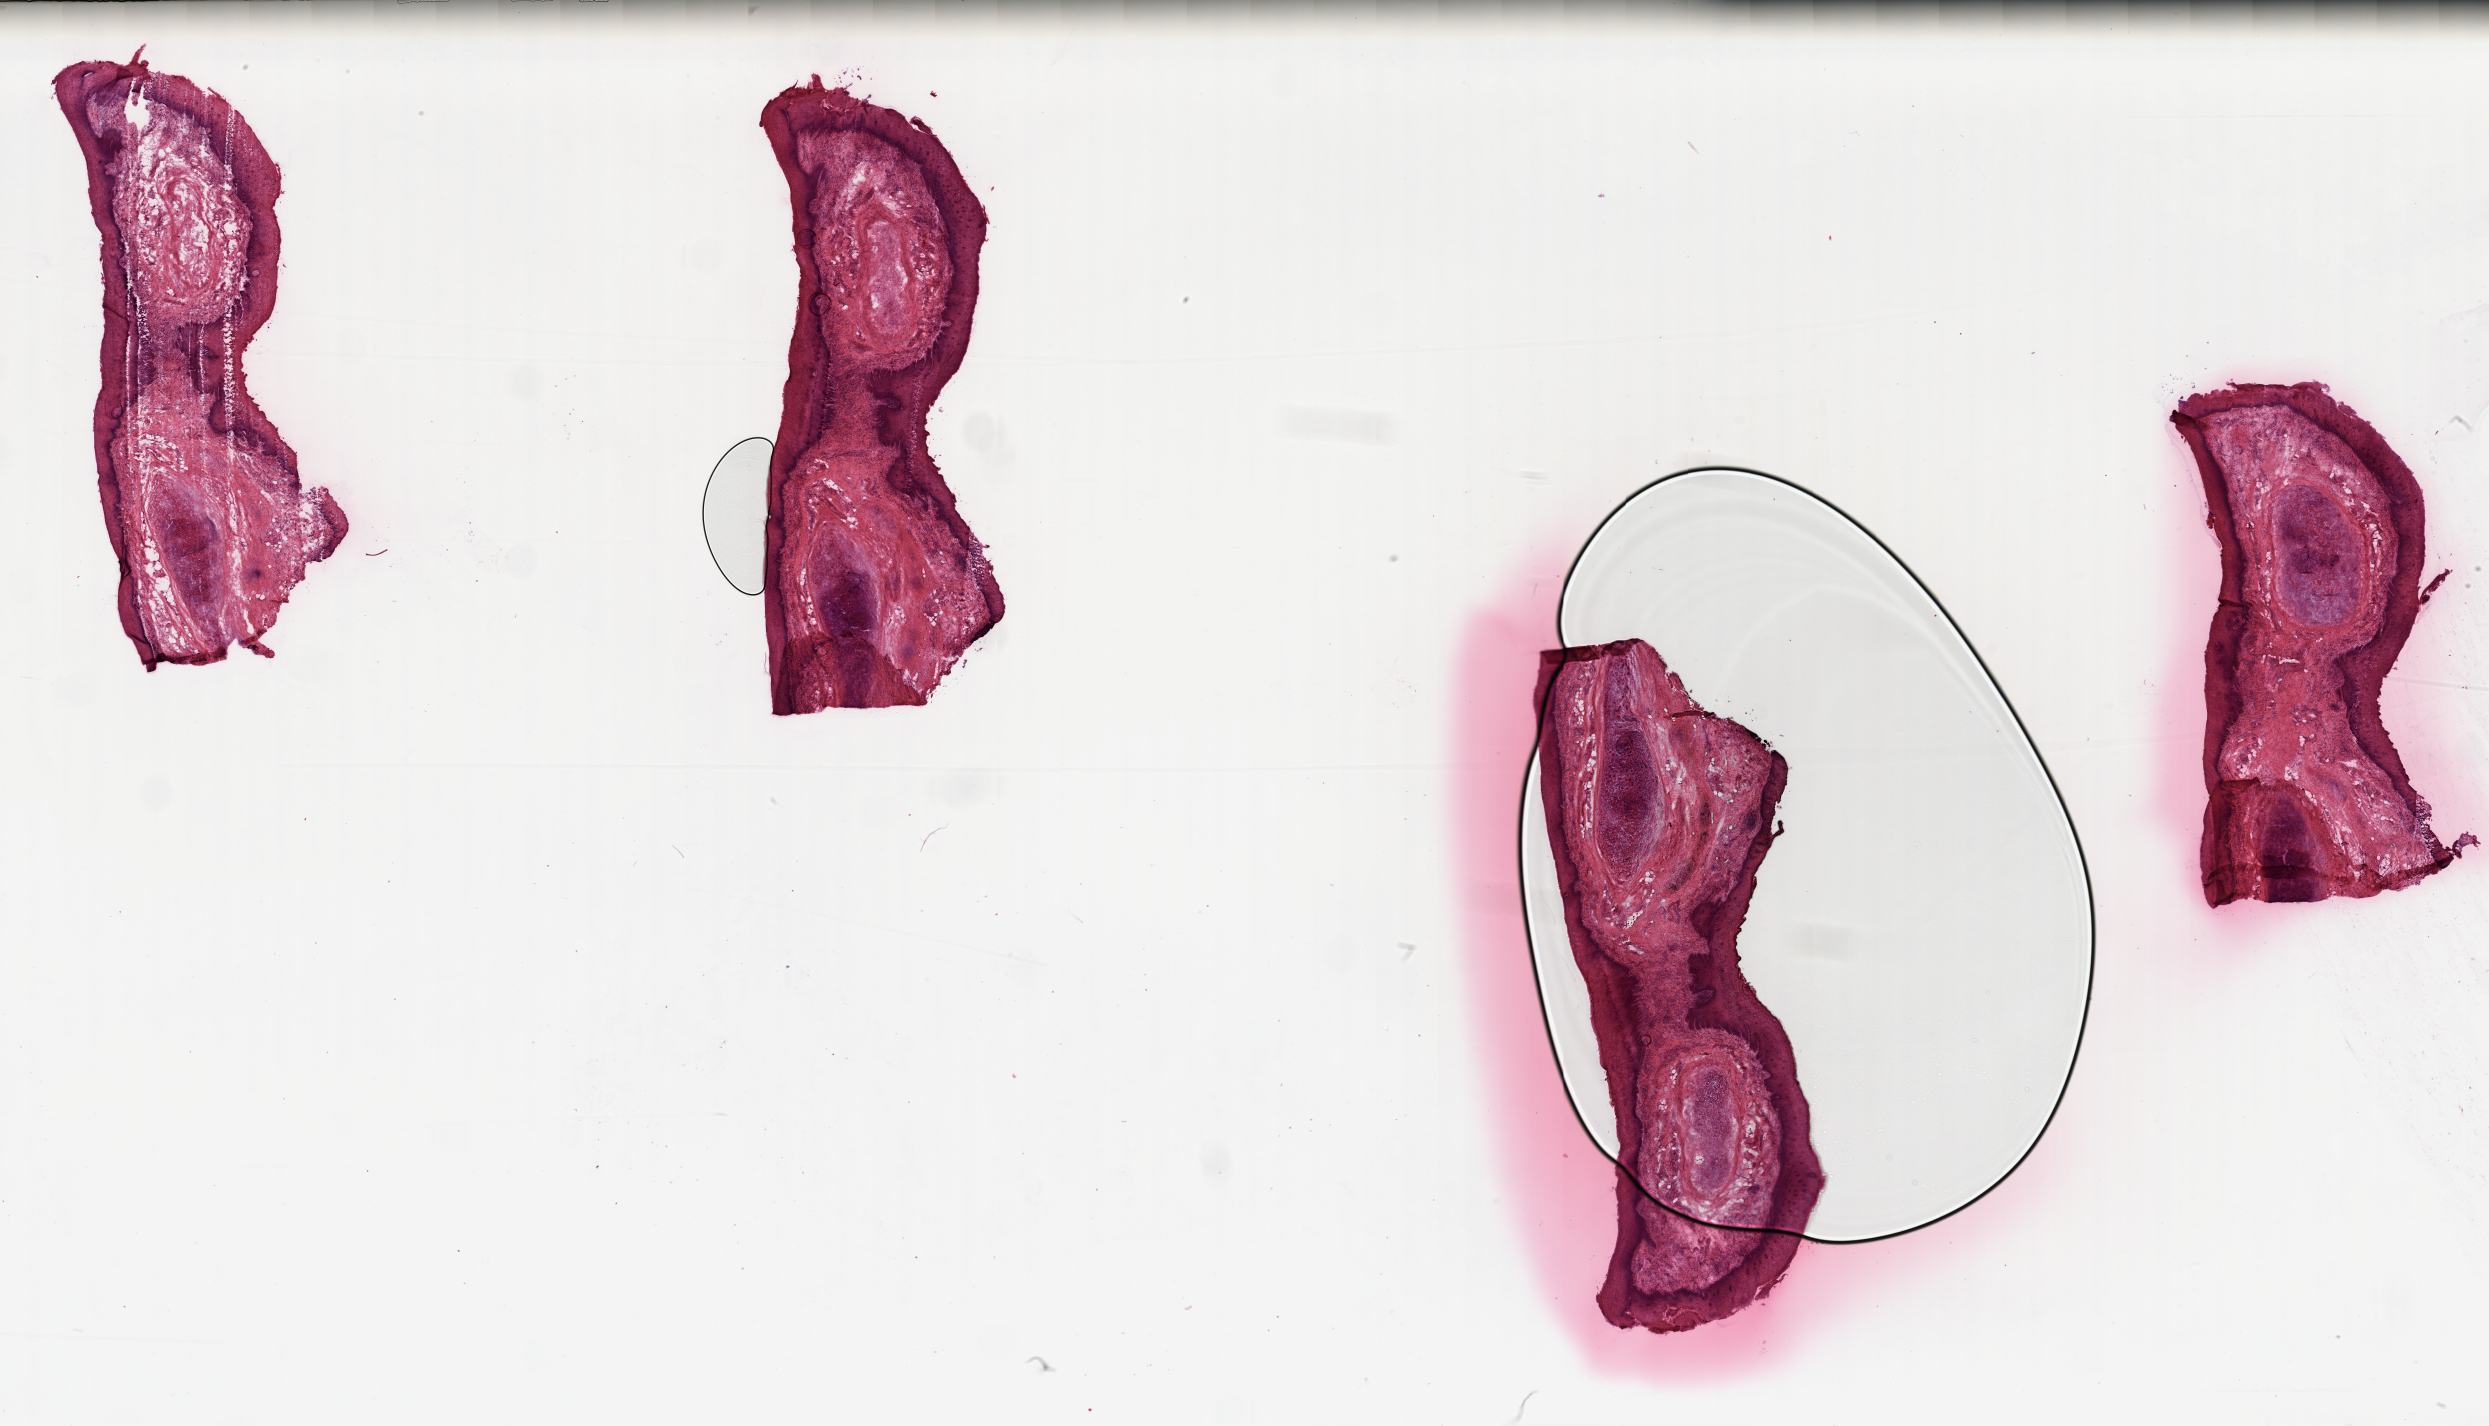
Digitized Hematoxylin and eosin (H&E) stained tissue section (whole slide), low-resolution overview of the scanned area, about 39.4 x 22.6 mm (acquisition: 20x scan), normal (non-tumour) tissue sample, sampled site: larynx. Male, 70 y/o.
This section: normal (non-tumour) tissue from the same patient. Patient diagnosis: Squamous cell carcinoma, NOS (larynx, NOS).